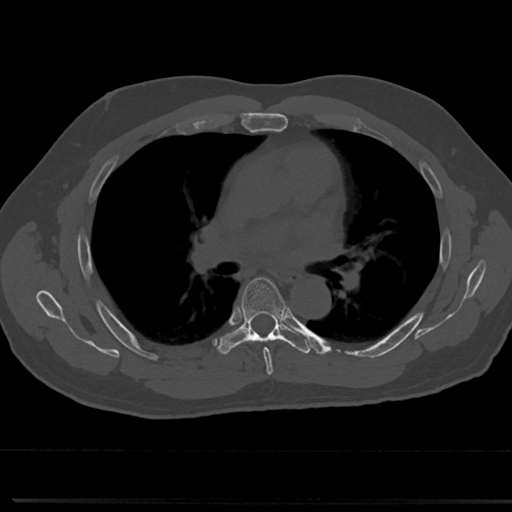
CT including the spine, one axial slice; slice 465 of 817 in the series (ordered by position); bone window (W 1800 / L 400 HU); 512 × 512 image matrix. Patient: male, 61 years. From the clinical record (not read from this slice): primary cancer: prostate.
Structures marked on this image (semi-automatic segmentation, software-assisted and operator-edited):
- T5 vertebra: bounding box (x1, y1, x2, y2) in pixels: (243, 279, 283, 364)
- T6 vertebra: (218, 275, 306, 354)